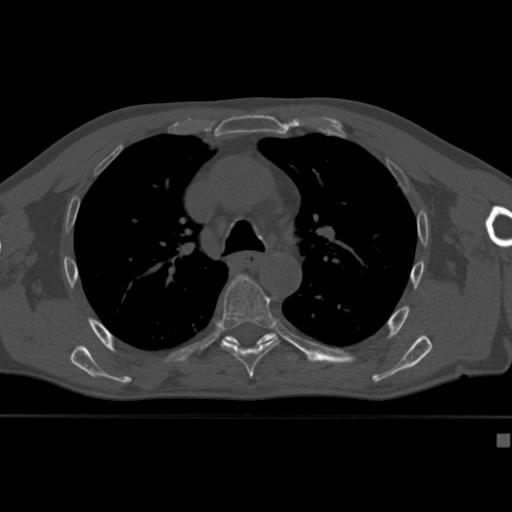
CT including the spine, one axial slice; slice 292 of 430 in the series (ordered by position); bone window (W 1800 / L 400 HU); 1.5 mm slice thickness; 512 × 512 image matrix, field of view 337 × 337 mm. Male patient, age 64 years. Case-level facts recorded for this patient, not image findings: primary cancer: uterus.
Structures marked on this image (semi-automatic segmentation, software-assisted and operator-edited):
- T6 vertebra: bounding box (x1, y1, x2, y2) in pixels: (219, 274, 280, 379)
- T7 vertebra: (224, 332, 299, 361)